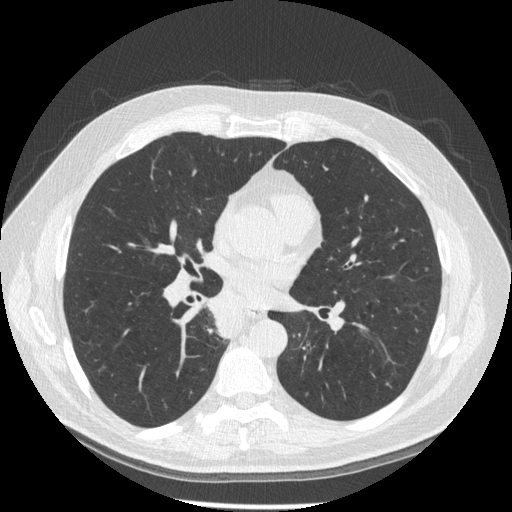
Axial slice from a low-dose chest CT screening exam. Third annual screen. Lung window (W 1500 / L -600 HU). 1.25 mm slice thickness. Standard (soft-tissue) reconstruction kernel (STANDARD). 120 kVp. Slice 88 of 181 in the series. Male participant, aged 61 years at enrolment. Former smoker at enrolment.
Expert reader's lesion annotation, box from (x=202, y=298) to (x=255, y=349) px. Screening reader's record for this exam: no non-calcified nodule ≥4 mm recorded. Official screen result: positive, other. Participant outcome: lung cancer diagnosed 10 days after this screen — squamous cell carcinoma, keratinizing, NOS, right lower lobe, stage IIIB (AJCC 6th edition), 40 mm at pathology.